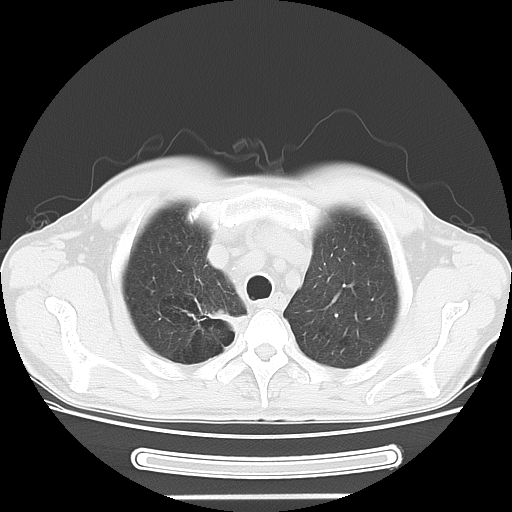
Chest CT, one axial slice. Slice 41 of 51 in the series (ordered by position). Reconstruction kernel LUNG. 120 kVp. Lung window (W 1500 / L -600 HU). 512 × 512 image matrix. Patient: male, 57 years. Case-level facts recorded for this patient, not image findings: clinical TNM (as recorded): T2 N3 M1b.
Annotated regions visible in this slice (bounding box drawn by a radiologist):
- lung tumour (recorded histology: adenocarcinoma): bounding box (x1, y1, x2, y2) in pixels: (199, 301, 243, 334)